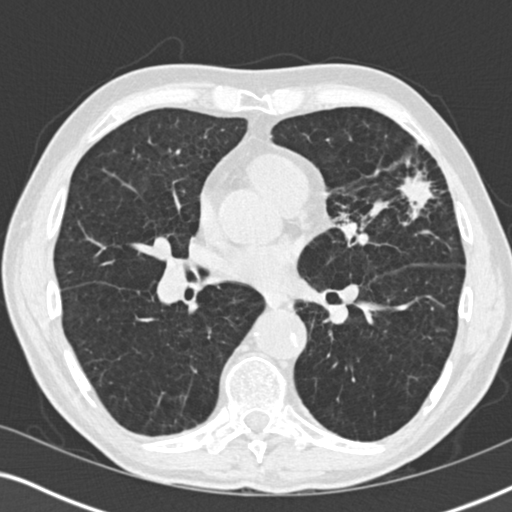
Low-dose screening chest CT, one axial slice; position 95 of 196 along the scan axis; 120 kVp; lung window (W 1500 / L -600 HU); 2 mm slice thickness; 512 × 512 image matrix.
Outlined on this slice (outlined manually by an expert reader):
- lesion 1 (tumor, upper lobe of left lung): bounding box [x1, y1, x2, y2] px = [400, 172, 434, 205]